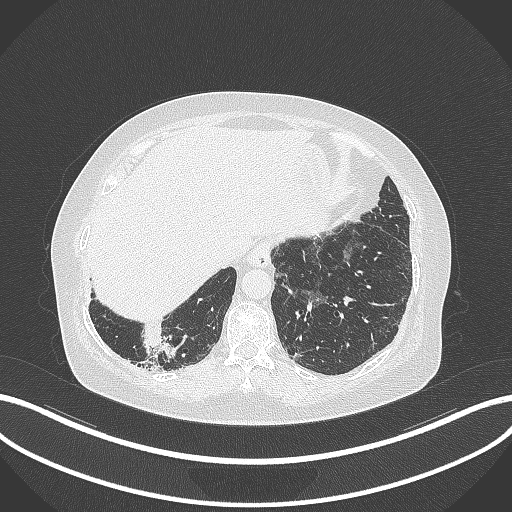
Chest CT, one axial slice; position 22 of 296 along the scan axis; reconstruction kernel B70f; lung window (W 1500 / L -600 HU); 512 × 512 image matrix, field of view 400 × 400 mm. Female patient, age 65 years. From the clinical record (not read from this slice): clinical TNM (as recorded): T2b N1 M0; histopathological grade: G1.
Outlined on this slice (bounding box drawn by a radiologist):
- lung tumour (recorded histology: adenocarcinoma): box from (x=139, y=324) to (x=179, y=364) px